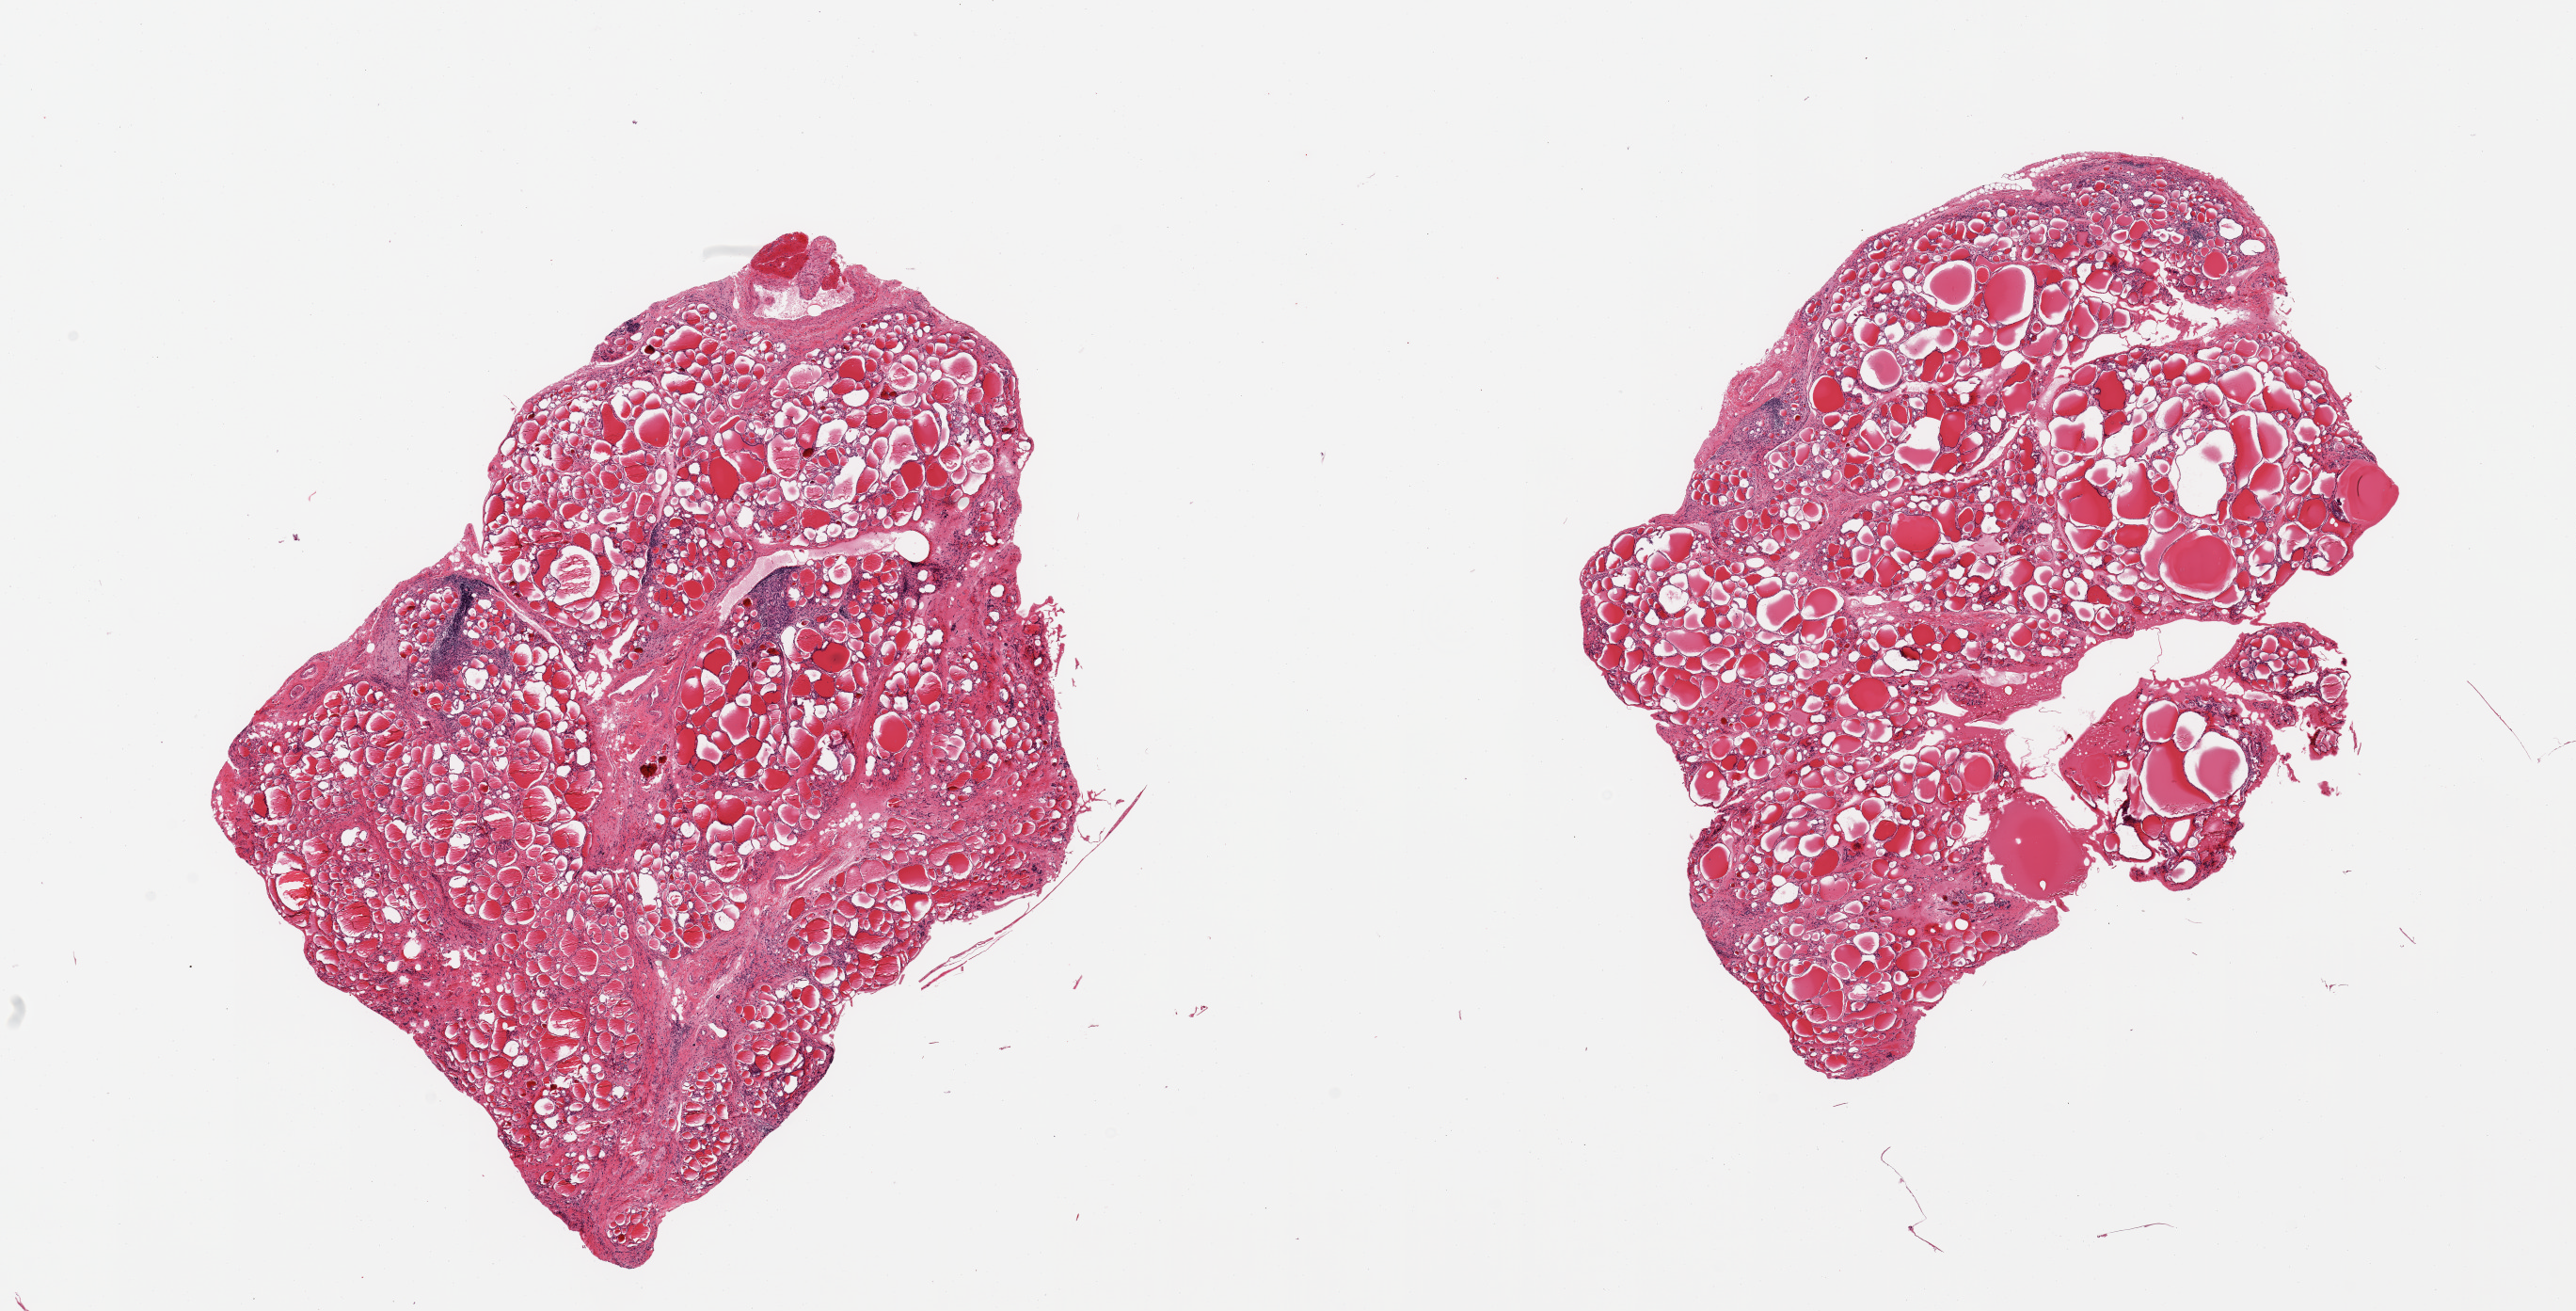
Whole-slide image, hematoxylin and eosin (H&E) stain, a low-resolution overview of the entire scanned area, about 21.7 x 11.0 mm (slide scanned at 20x); PAXgene-fixed paraffin-embedded (PFPE) section; sampled site (target tissue): thyroid; donor tissue sample. Female donor.
Review note (as recorded): 2 pieces, mild regressive changes.